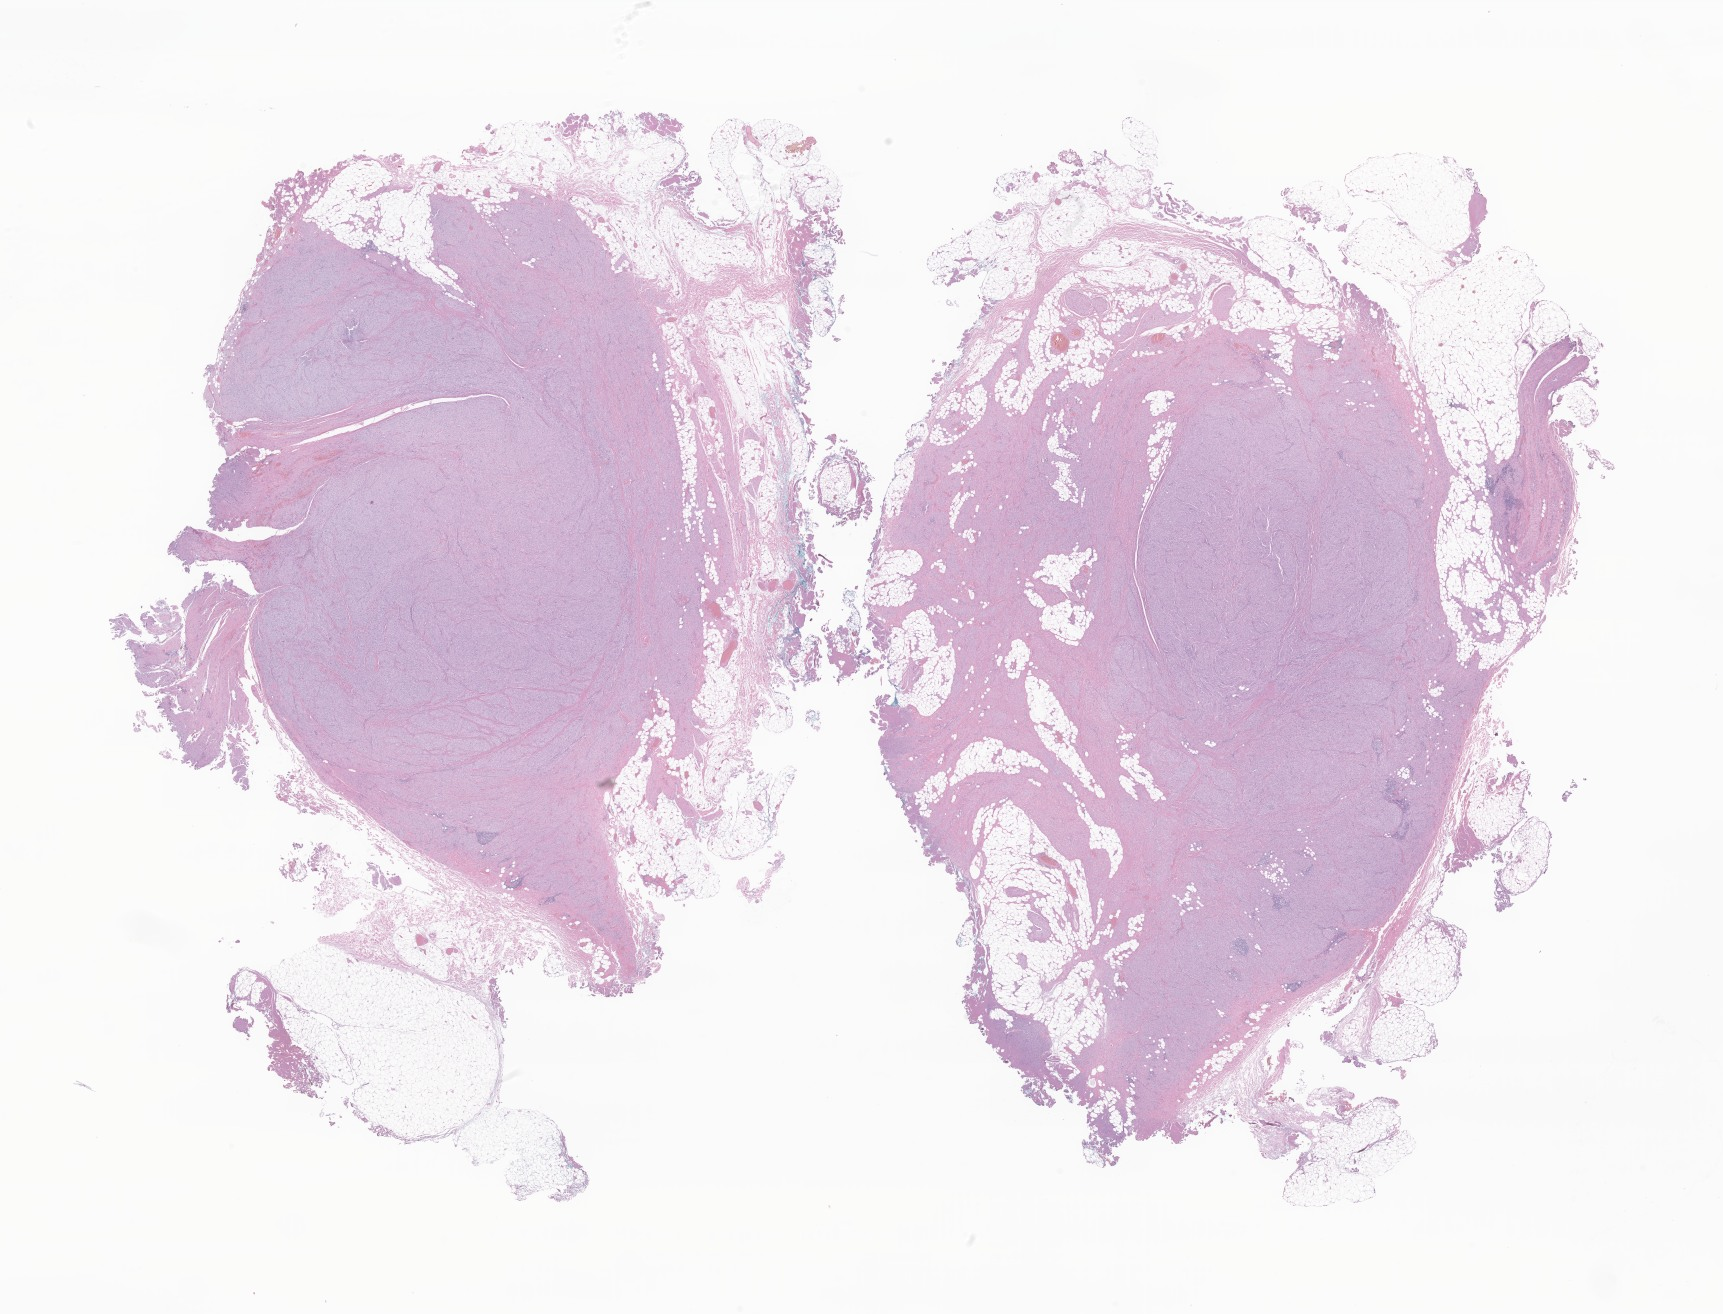
Digitized hematoxylin and eosin (H&E)-stained section of tumor tissue from the lung, shown as a low-resolution overview of the whole scanned area (about 29.1 x 22.2 mm), formalin-fixed, paraffin-embedded (FFPE) tissue. Patient: female, age 180 months.
Recorded diagnosis: Sarcoma, NOS.